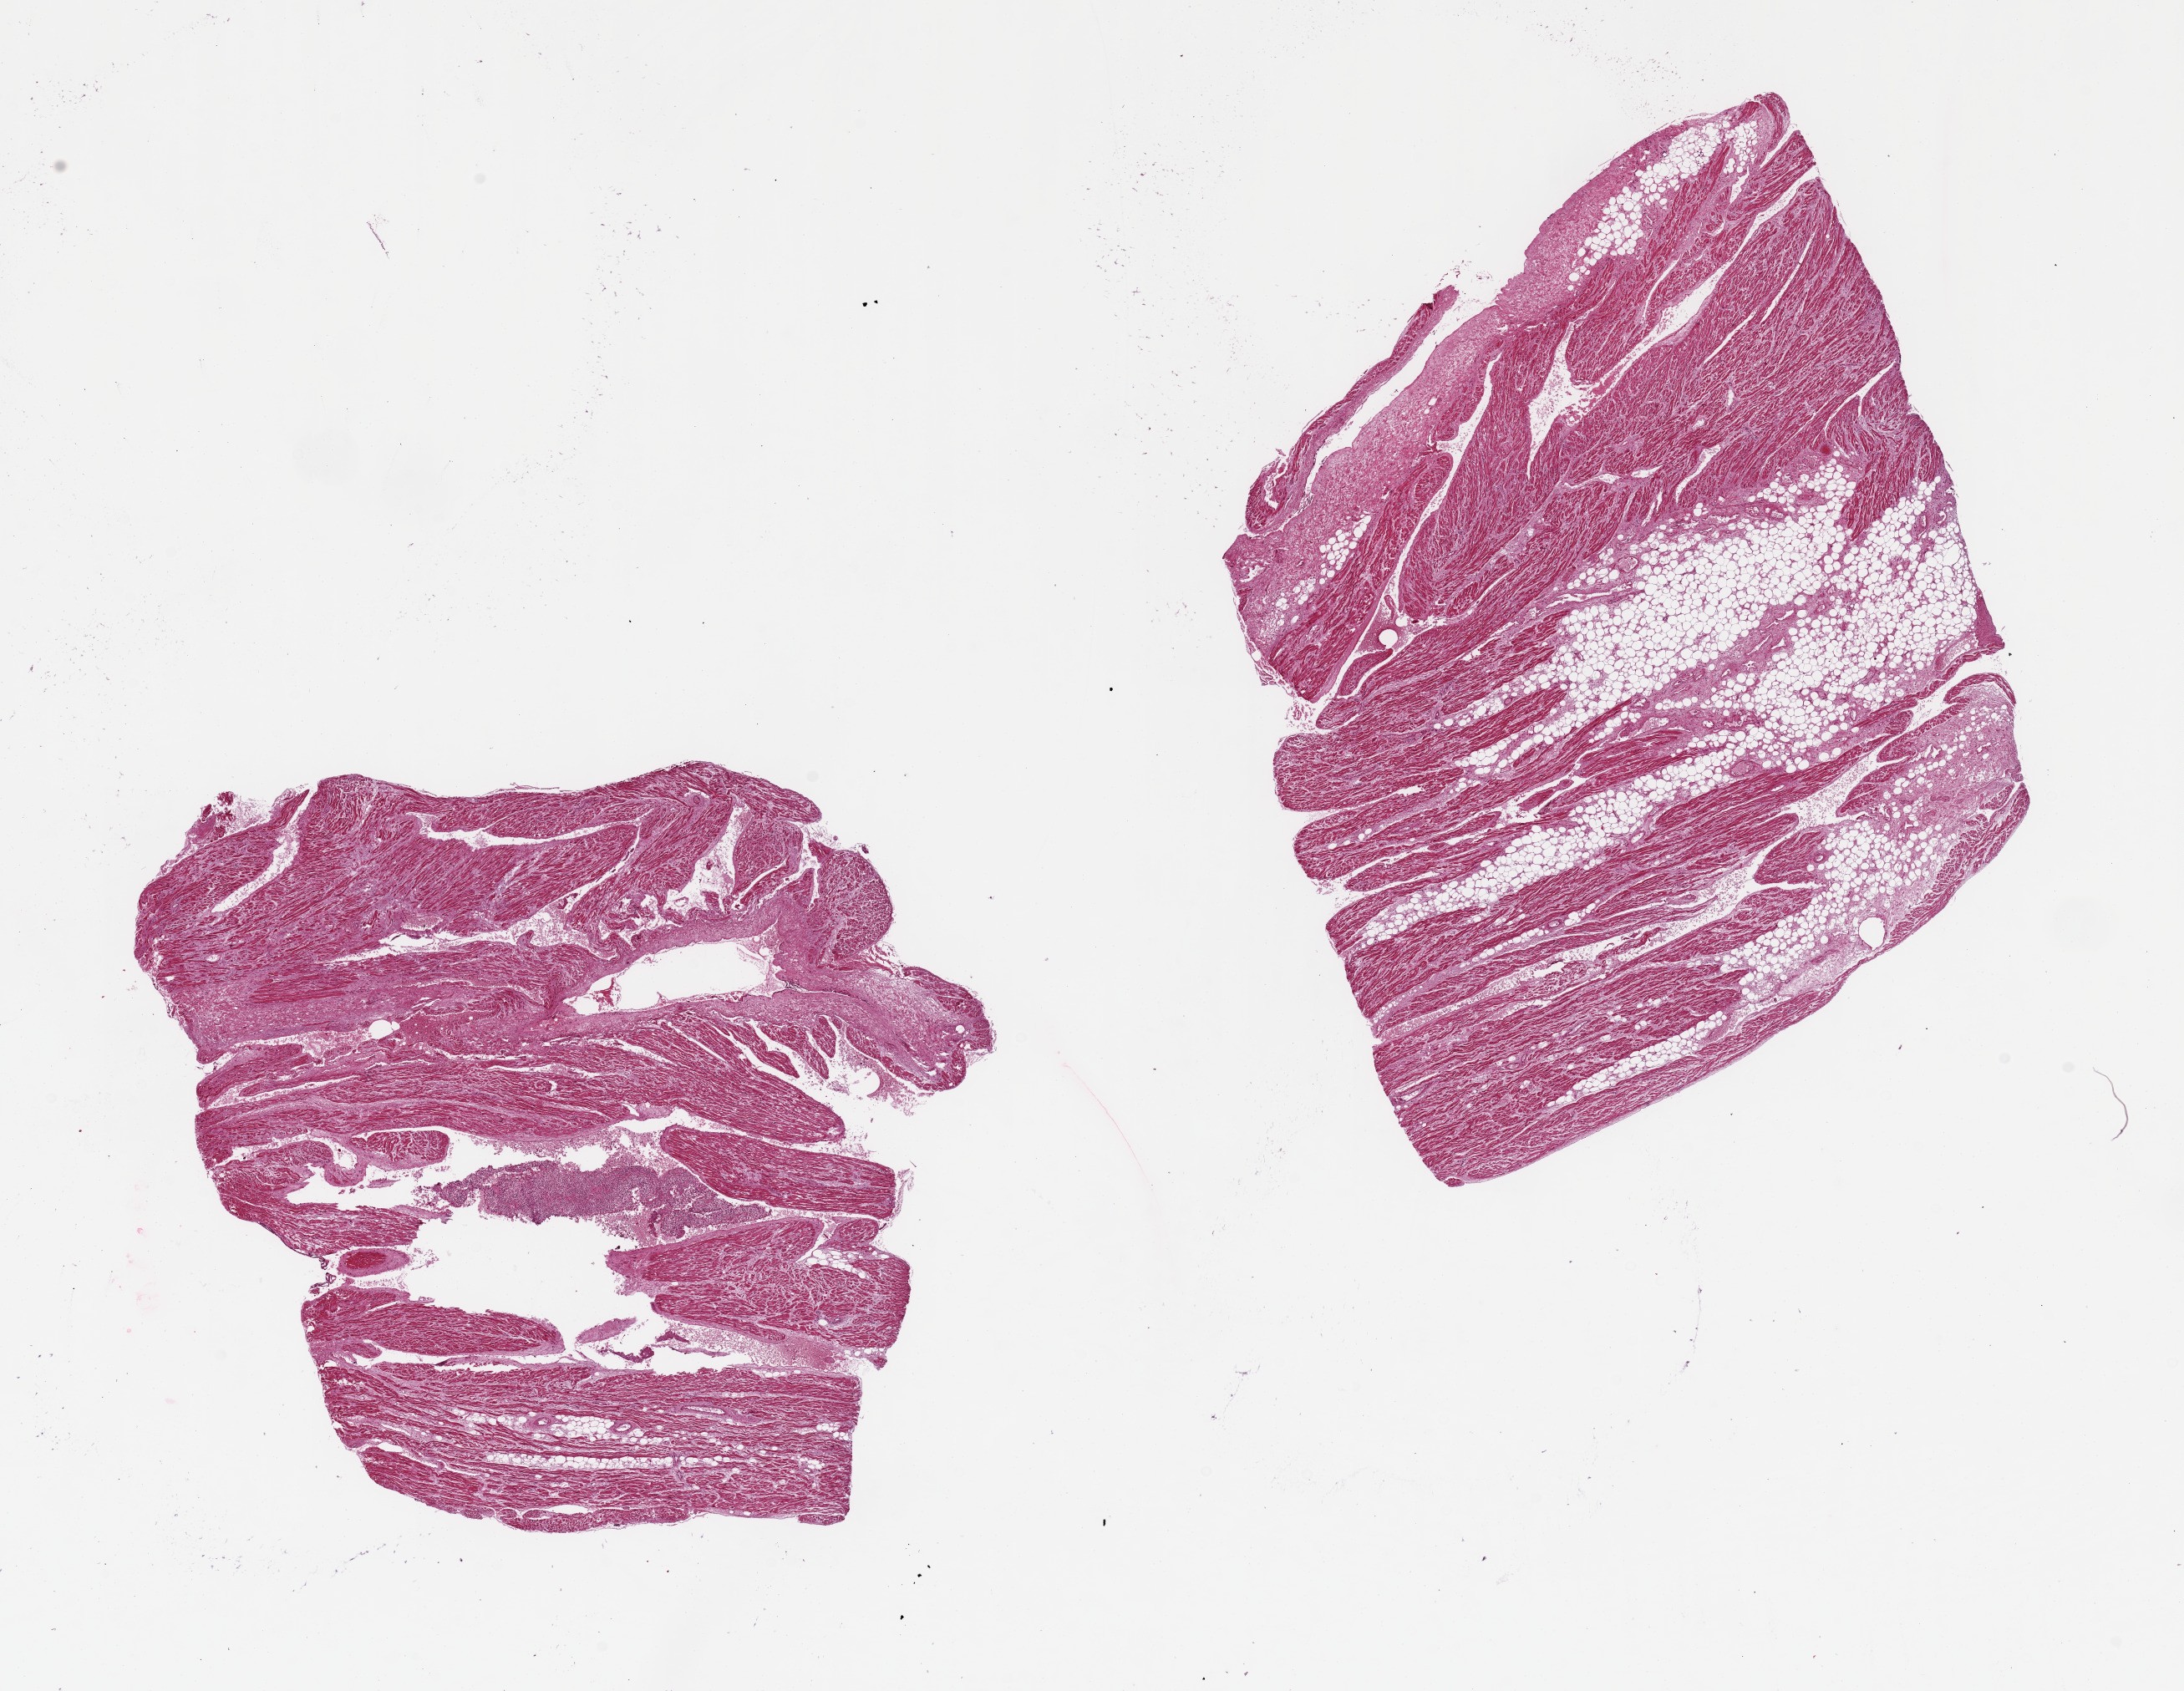
Whole-slide image, H&E stain — shown as a low-resolution overview of the whole scanned area (about 20.7 x 16.0 mm). PAXgene-fixed paraffin-embedded (PFPE) section. Target tissue: auricular appendage. Tissue donor sample. Female donor.
- reviewer comment on this tissue sample: 2 pieces, 8x7 & 8x7mm